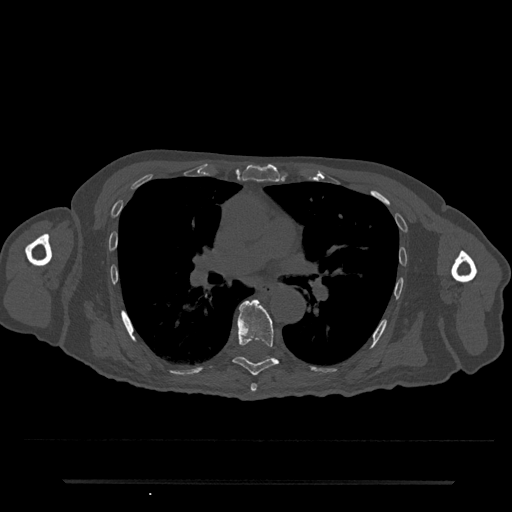
CT including the spine, one axial slice. Slice 477 of 797 in the series (ordered by position). Bone window (W 1800 / L 400 HU). 0.5 mm slice thickness. 512 × 512 image matrix. Male patient, age 74 years. From the clinical record (not read from this slice): primary cancer: prostate.
Annotated regions visible in this slice (semi-automatically segmented with operator editing):
- T6 vertebra: box from (x=250, y=384) to (x=257, y=392) px
- T7 vertebra: (x=233, y=300)–(x=279, y=376)
- T8 vertebra: (x=265, y=356)–(x=273, y=360)